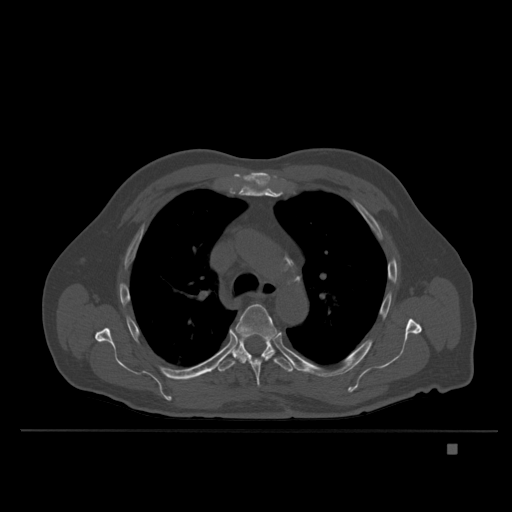
CT including the spine, one axial slice; position 268 of 435 along the scan axis; bone window (W 1800 / L 400 HU); 1.5 mm slice thickness; 512 × 512 image matrix, field of view 434 × 434 mm. Male patient, age 73 years. Case-level facts recorded for this patient, not image findings: primary cancer: skin.
Structures marked on this image (semi-automatically segmented with operator editing):
- T3 vertebra: bounding box (x1, y1, x2, y2) in pixels: (267, 354, 272, 360)
- T5 vertebra: (233, 304, 281, 387)
- T6 vertebra: (217, 334, 294, 373)
- T7 vertebra: (234, 338, 239, 349)